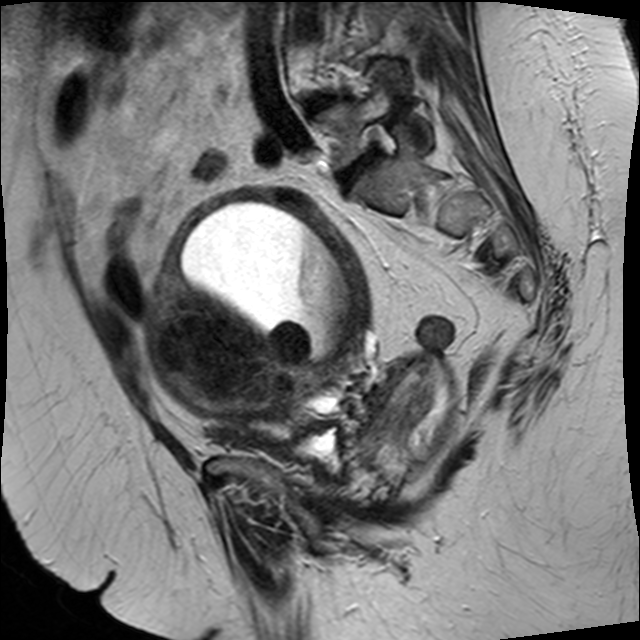
Pelvic MRI for cervical cancer, one sagittal slice; slice 22 of 34 in the series (ordered by position); T2-weighted; 1.5 T; TE 89 ms, TR 3320 ms; 4 mm slice thickness; 640 × 640 image matrix. Female patient, age 50 years.
Annotated regions visible in this slice (manually delineated by an expert):
- uterus and cervix: bounding box [x1, y1, x2, y2] px = [149, 188, 445, 476]